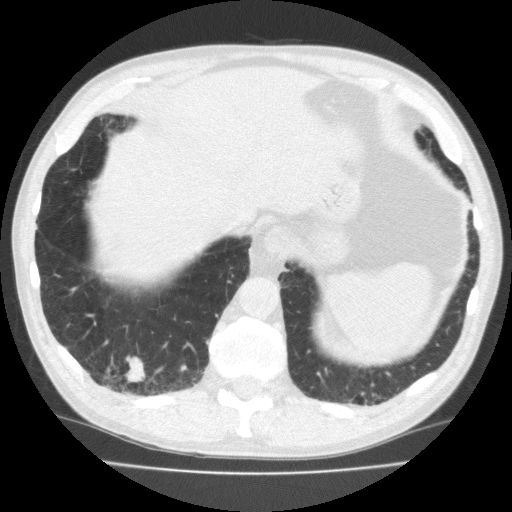
Chest CT (low-dose screening protocol), one axial image. Second annual screen. Lung window (W 1500 / L -600 HU). 512 × 512 image matrix. Male participant, aged 70 years at enrolment.
Expert reader's lesion annotation, bounding box (x1, y1, x2, y2) in pixels: (91, 347, 159, 399). Screening reader's record for this exam (one nodule recorded; not confirmed to be the boxed lesion): non-calcified nodule or mass ≥4 mm, right lower lobe, 18 × 13 mm, spiculated (stellate) margins, soft tissue attenuation, pre-existing on the prior screen: no.